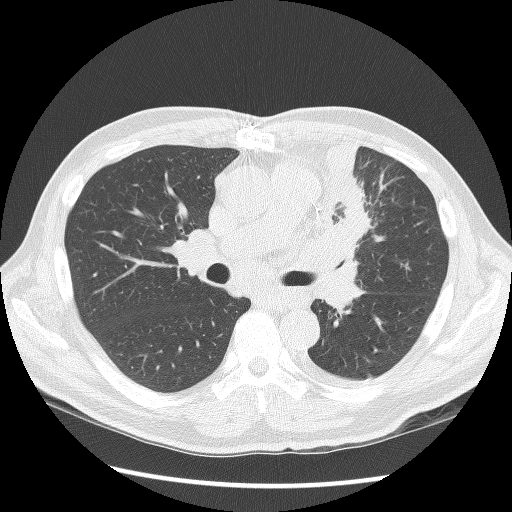
Axial slice from a low-dose chest CT screening exam; second screening round (one year after baseline); lung window (W 1500 / L -600 HU); 512 × 512 image matrix. Male, age 64 years at enrolment. Former smoker at enrolment.
Expert-annotated lung lesion, bounding box <303,142,386,282> (left, top, right, bottom; pixels). No non-calcified nodule or mass ≥4 mm was recorded by the screening reader at this exam.